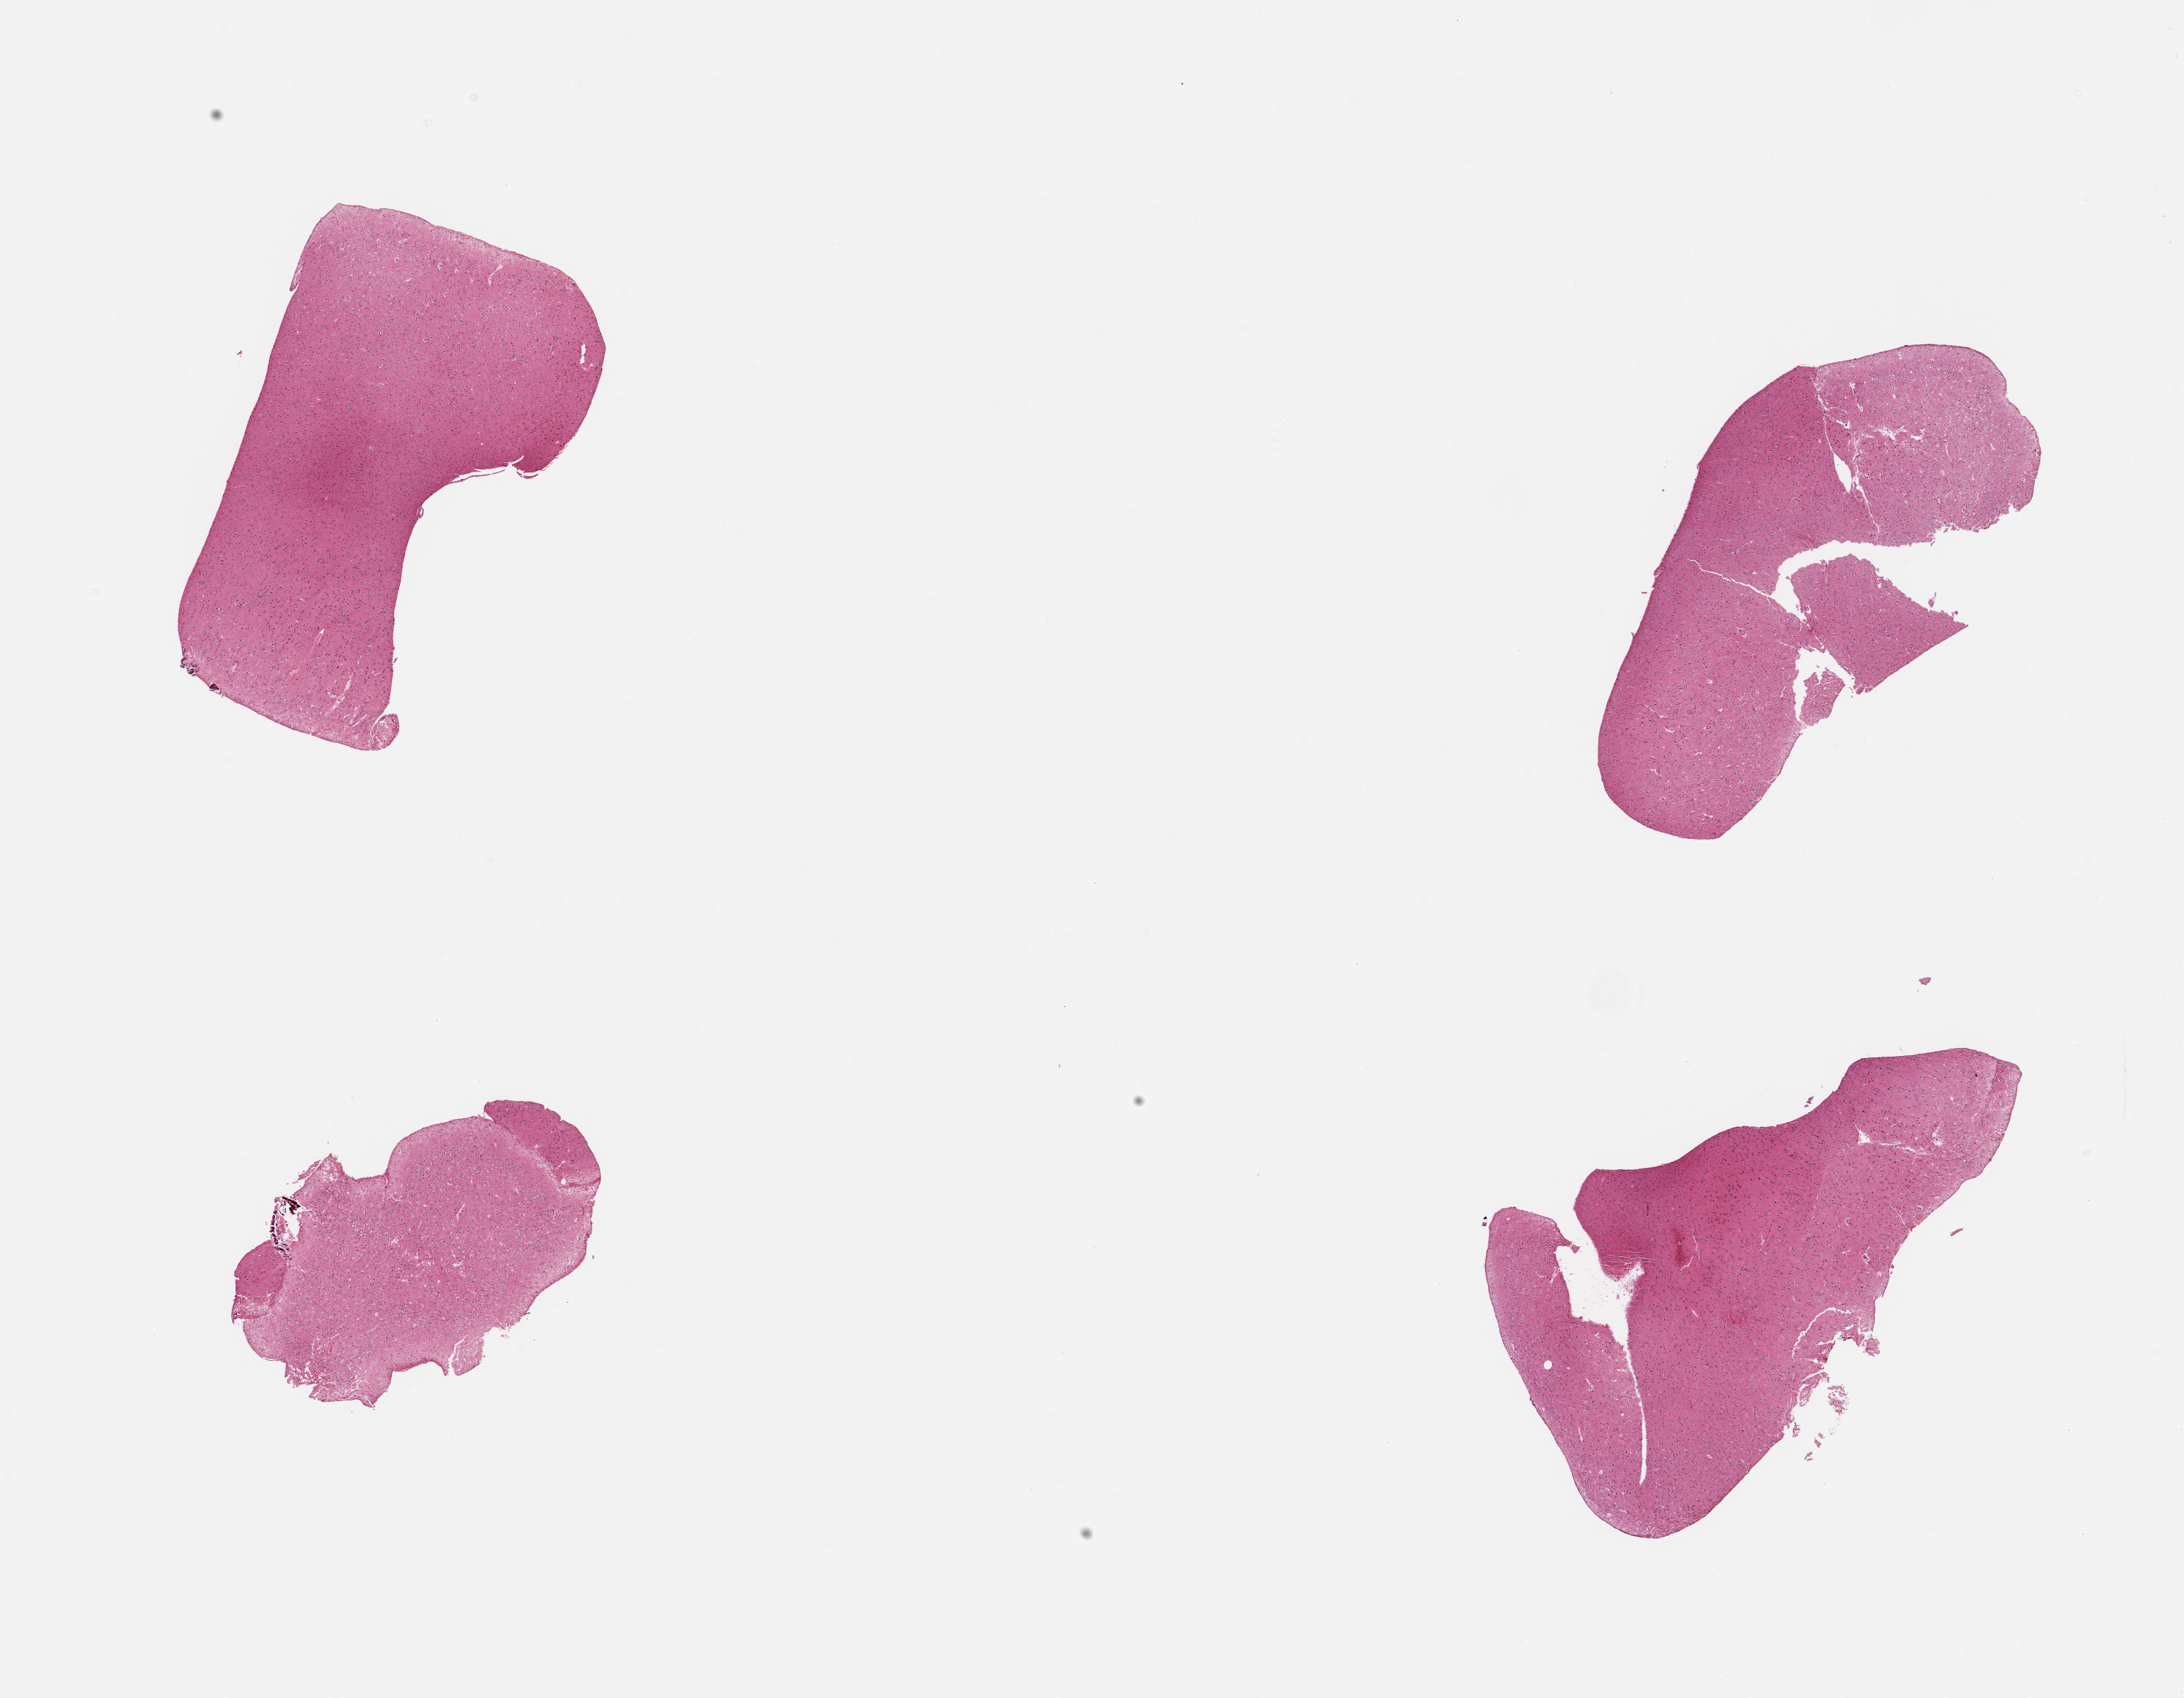
Digitized hematoxylin and eosin (H&E)-stained section, low-resolution overview of the scanned area, about 23.6 x 18.4 mm. PAXgene-fixed paraffin-embedded (PFPE) section. Target tissue: cerebral cortex. Tissue donor sample. Donor: female.
Pathologist's review note for this sample: 4 pieces.